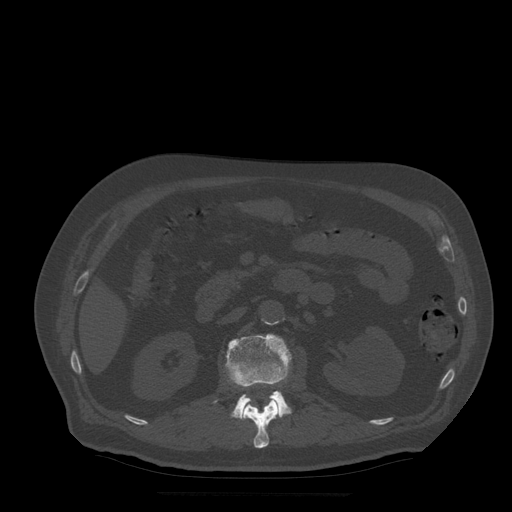
CT including the spine, one axial slice. Position 182 of 522 along the scan axis. Bone window (W 1800 / L 400 HU). 1.25 mm slice thickness. 512 × 512 image matrix, field of view 420 × 420 mm. Patient age 72 years. Case-level facts recorded for this patient, not image findings: primary cancer: prostate.
Outlined on this slice (semi-automatic segmentation, software-assisted and operator-edited):
- L1 vertebra: bounding box (x1, y1, x2, y2) in pixels: (241, 383, 279, 449)
- L2 vertebra: (215, 334, 292, 420)